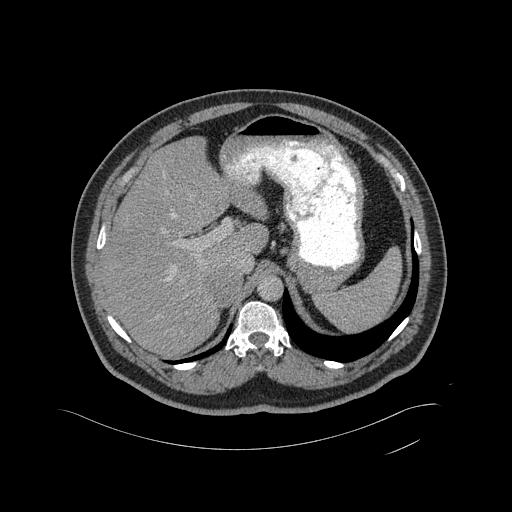
Contrast-enhanced abdominal CT, one axial slice. Slice 339 of 433 in the series (ordered by position). Intravenous contrast given. Soft-tissue window (W 400 / L 40 HU). 2 mm slice thickness. 512 × 512 image matrix. Patient: male, 56 years. From the clinical record (not read from this slice): diagnosis: adrenocortical carcinoma; tumour side: right adrenal; tumour size at pathology: 11.6 cm; Ki-67 index: 50 %; stage (as recorded): 3.
Annotated regions visible in this slice (semi-automatically segmented with operator editing):
- mass: box from (x=207, y=267) to (x=240, y=302) px